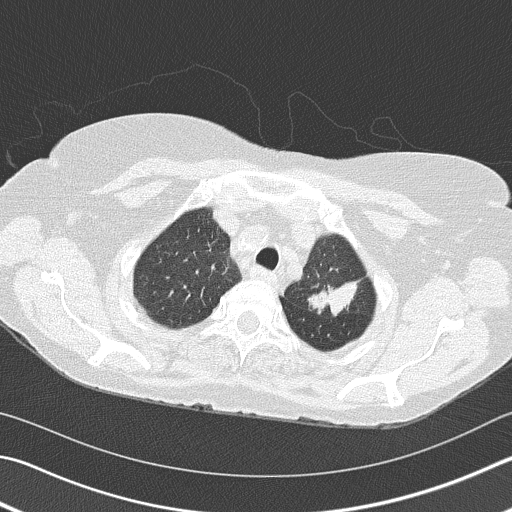
Low-dose screening chest CT, axial slice; second screening round (one year after baseline); lung window (W 1500 / L -600 HU); lung (sharp) reconstruction kernel (B50f); 120 kVp; 512 × 512 image matrix, field of view 342 × 342 mm. Female, age 68 years at enrolment.
Expert reader's lesion annotation, bounding box (x1, y1, x2, y2) in pixels: (290, 241, 372, 328). Reader record for this screening exam (exam-level; its link to the box is not recorded): non-calcified nodule or mass ≥4 mm, left upper lobe, 4 × 2 mm, spiculated (stellate) margins, soft tissue attenuation, pre-existing on the prior screen: yes; interval growth: yes. Lung cancer was diagnosed 392 days after this screen: adenocarcinoma, NOS, left upper lobe, poorly differentiated (G3), stage IB (AJCC 6th edition), 50 mm at pathology.